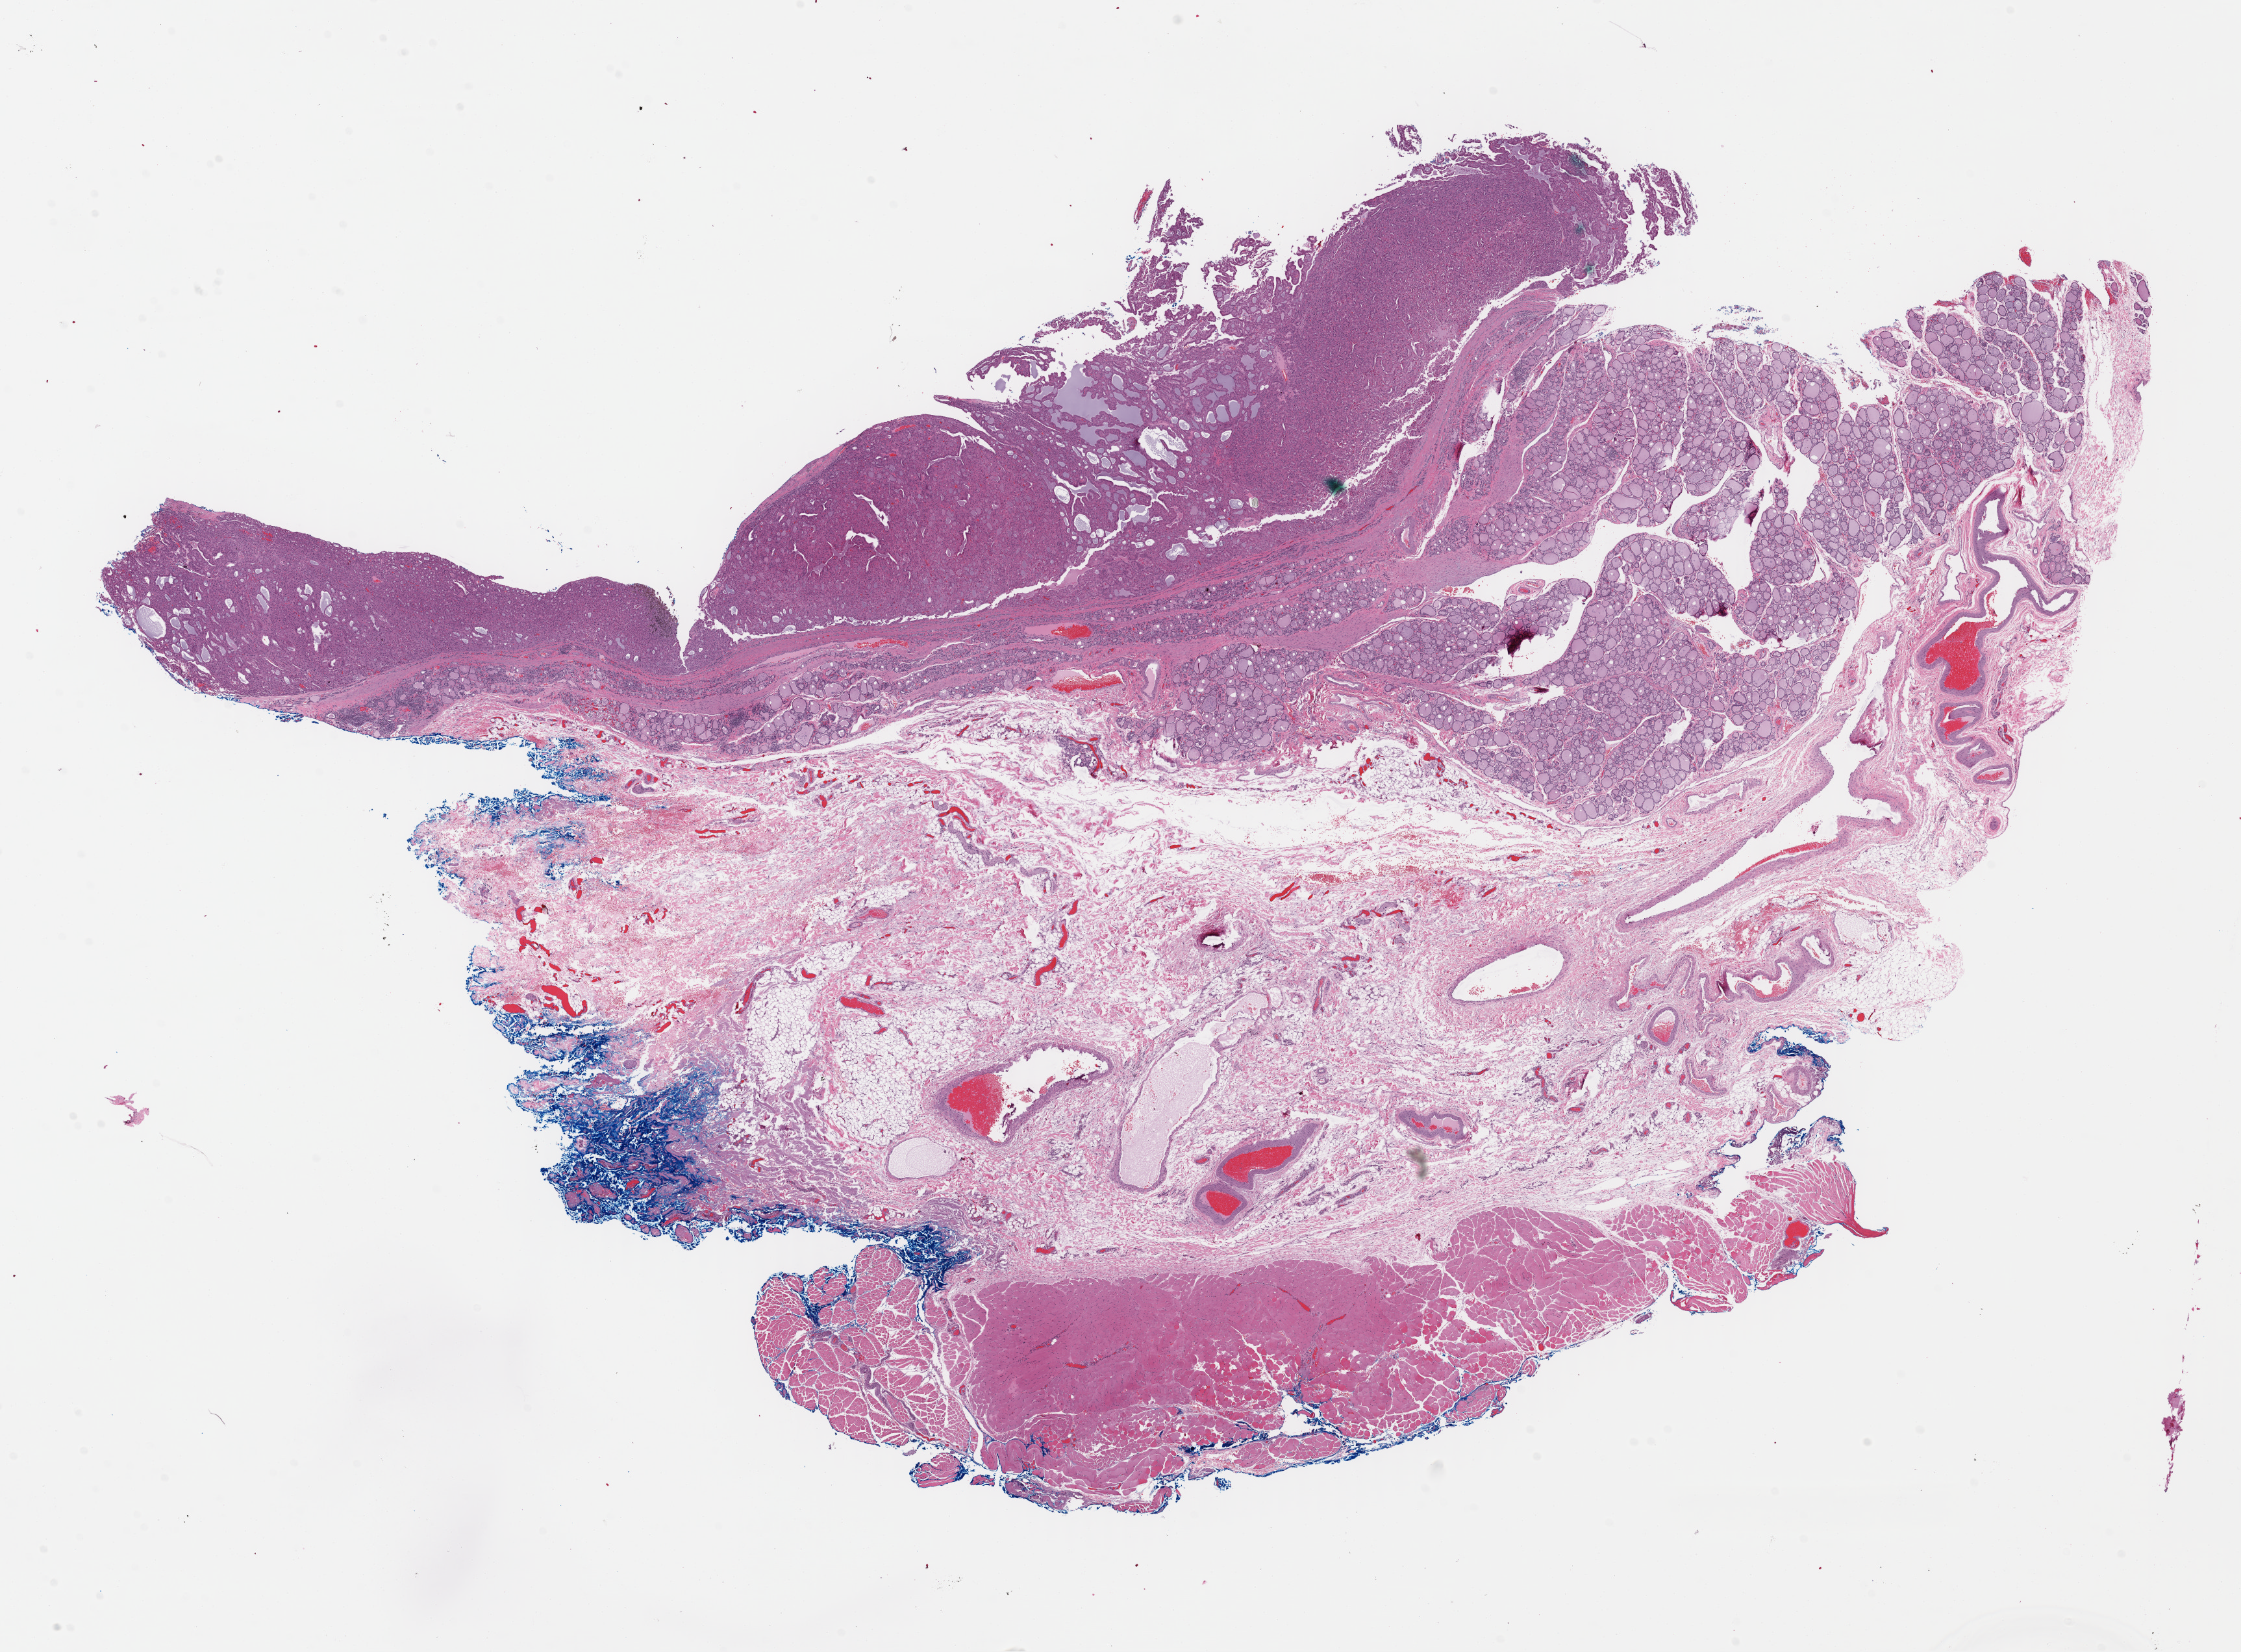
H&E-stained whole-slide image — a low-resolution overview of the entire scanned area, about 27.1 x 20.0 mm (from a 40x scan). Formalin-fixed paraffin-embedded (FFPE) diagnostic section. Primary tumour sample from the thyroid. Female patient; age at initial diagnosis 57 years.
* TNM: T2 N0 M0
* AJCC pathologic stage: II (7th edition)
* laterality: right
* lymph nodes positive (case pathology): 0 of 4 examined
* pathologic diagnosis: Papillary adenocarcinoma, NOS (thyroid gland)